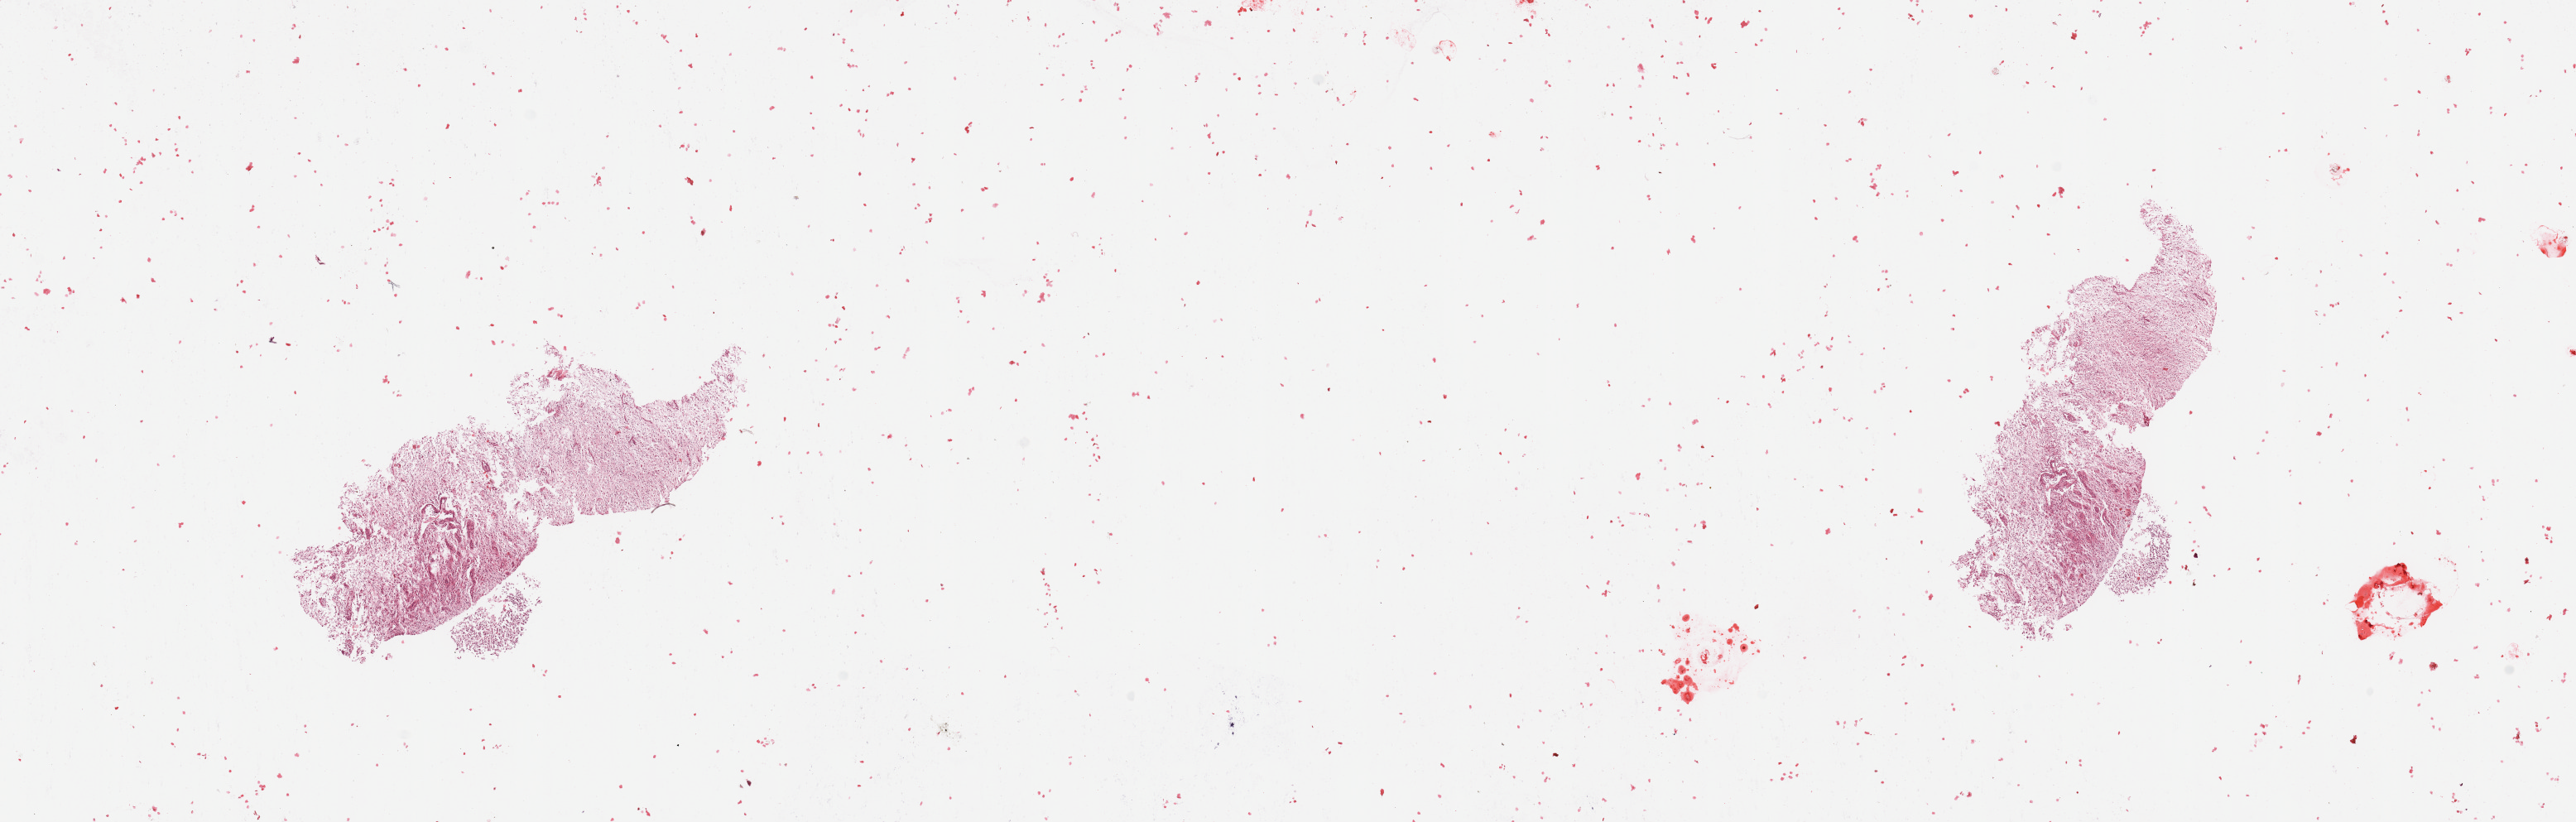
H&E-stained whole-slide image — a low-resolution overview of the entire scanned area, about 24.6 x 7.9 mm; tumour tissue sample, sampled site: frontal lobe. Patient: male, age 63 years. Pathologist review of this section (percent, as recorded): tumour nuclei 65%, necrosis 15%.
Histologic diagnosis: Glioblastoma.